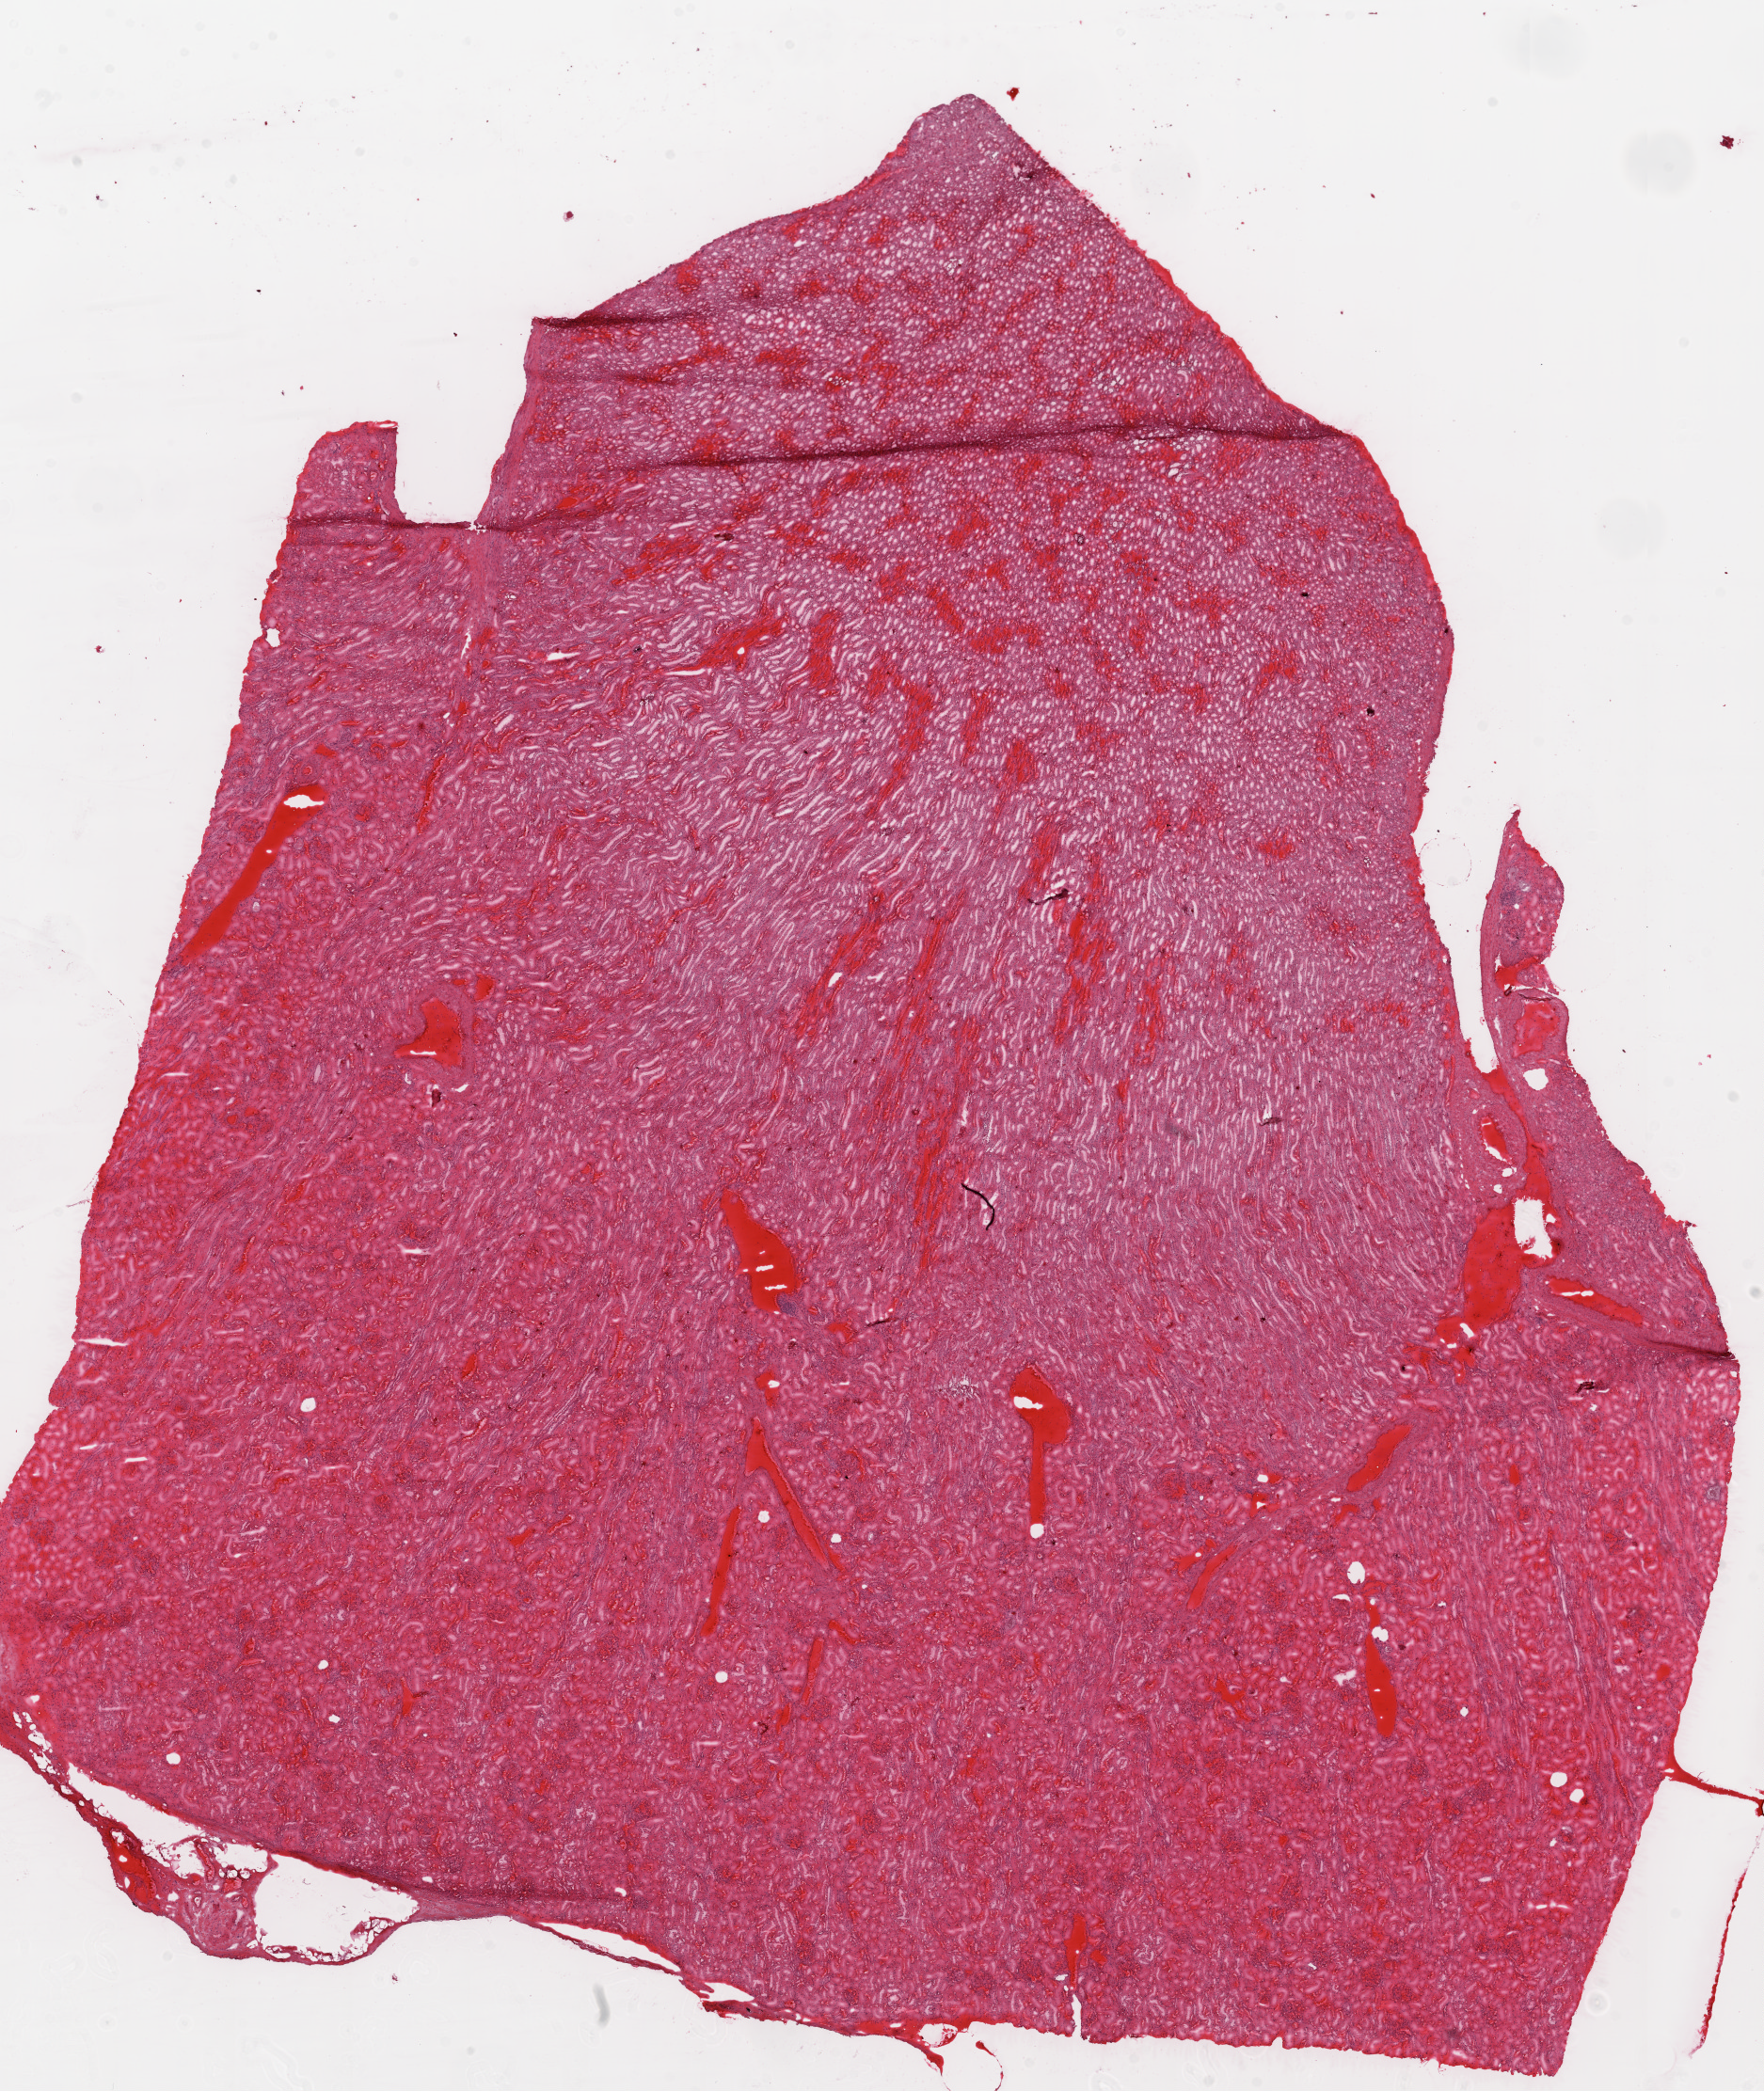
Digitized H&E-stained tissue section (whole slide) — low-resolution overview of the scanned area, about 15.0 x 17.8 mm; frozen section from the top of the tissue portion; solid tissue normal (non-tumour tissue) sample from the kidney. Patient: male, age at initial diagnosis 44 years.
* this section: solid tissue normal sample (biorepository sample class)
* patient diagnosis: Clear cell adenocarcinoma, NOS